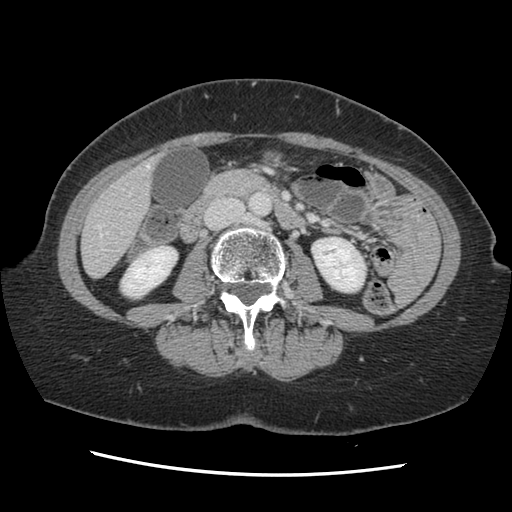
Contrast-enhanced abdominal CT, one axial slice; position 41 of 141 along the scan axis; soft-tissue window (W 400 / L 40 HU); 2.5 mm slice thickness; 512 × 512 image matrix, field of view 330 × 330 mm. Female patient, age 61 years. From the clinical record (not read from this slice): diagnosis: colorectal cancer liver metastases, imaged before liver resection; multiple liver metastases: no; largest metastasis: 2.4 cm; disease in both lobes: no.
Structures marked on this image (expert manual segmentation):
- hepatic veins: bounding box [x1, y1, x2, y2] px = [97, 163, 150, 236]
- liver: [83, 162, 155, 277]
- planned liver remnant (the part of the liver to remain after resection): [83, 169, 153, 277]